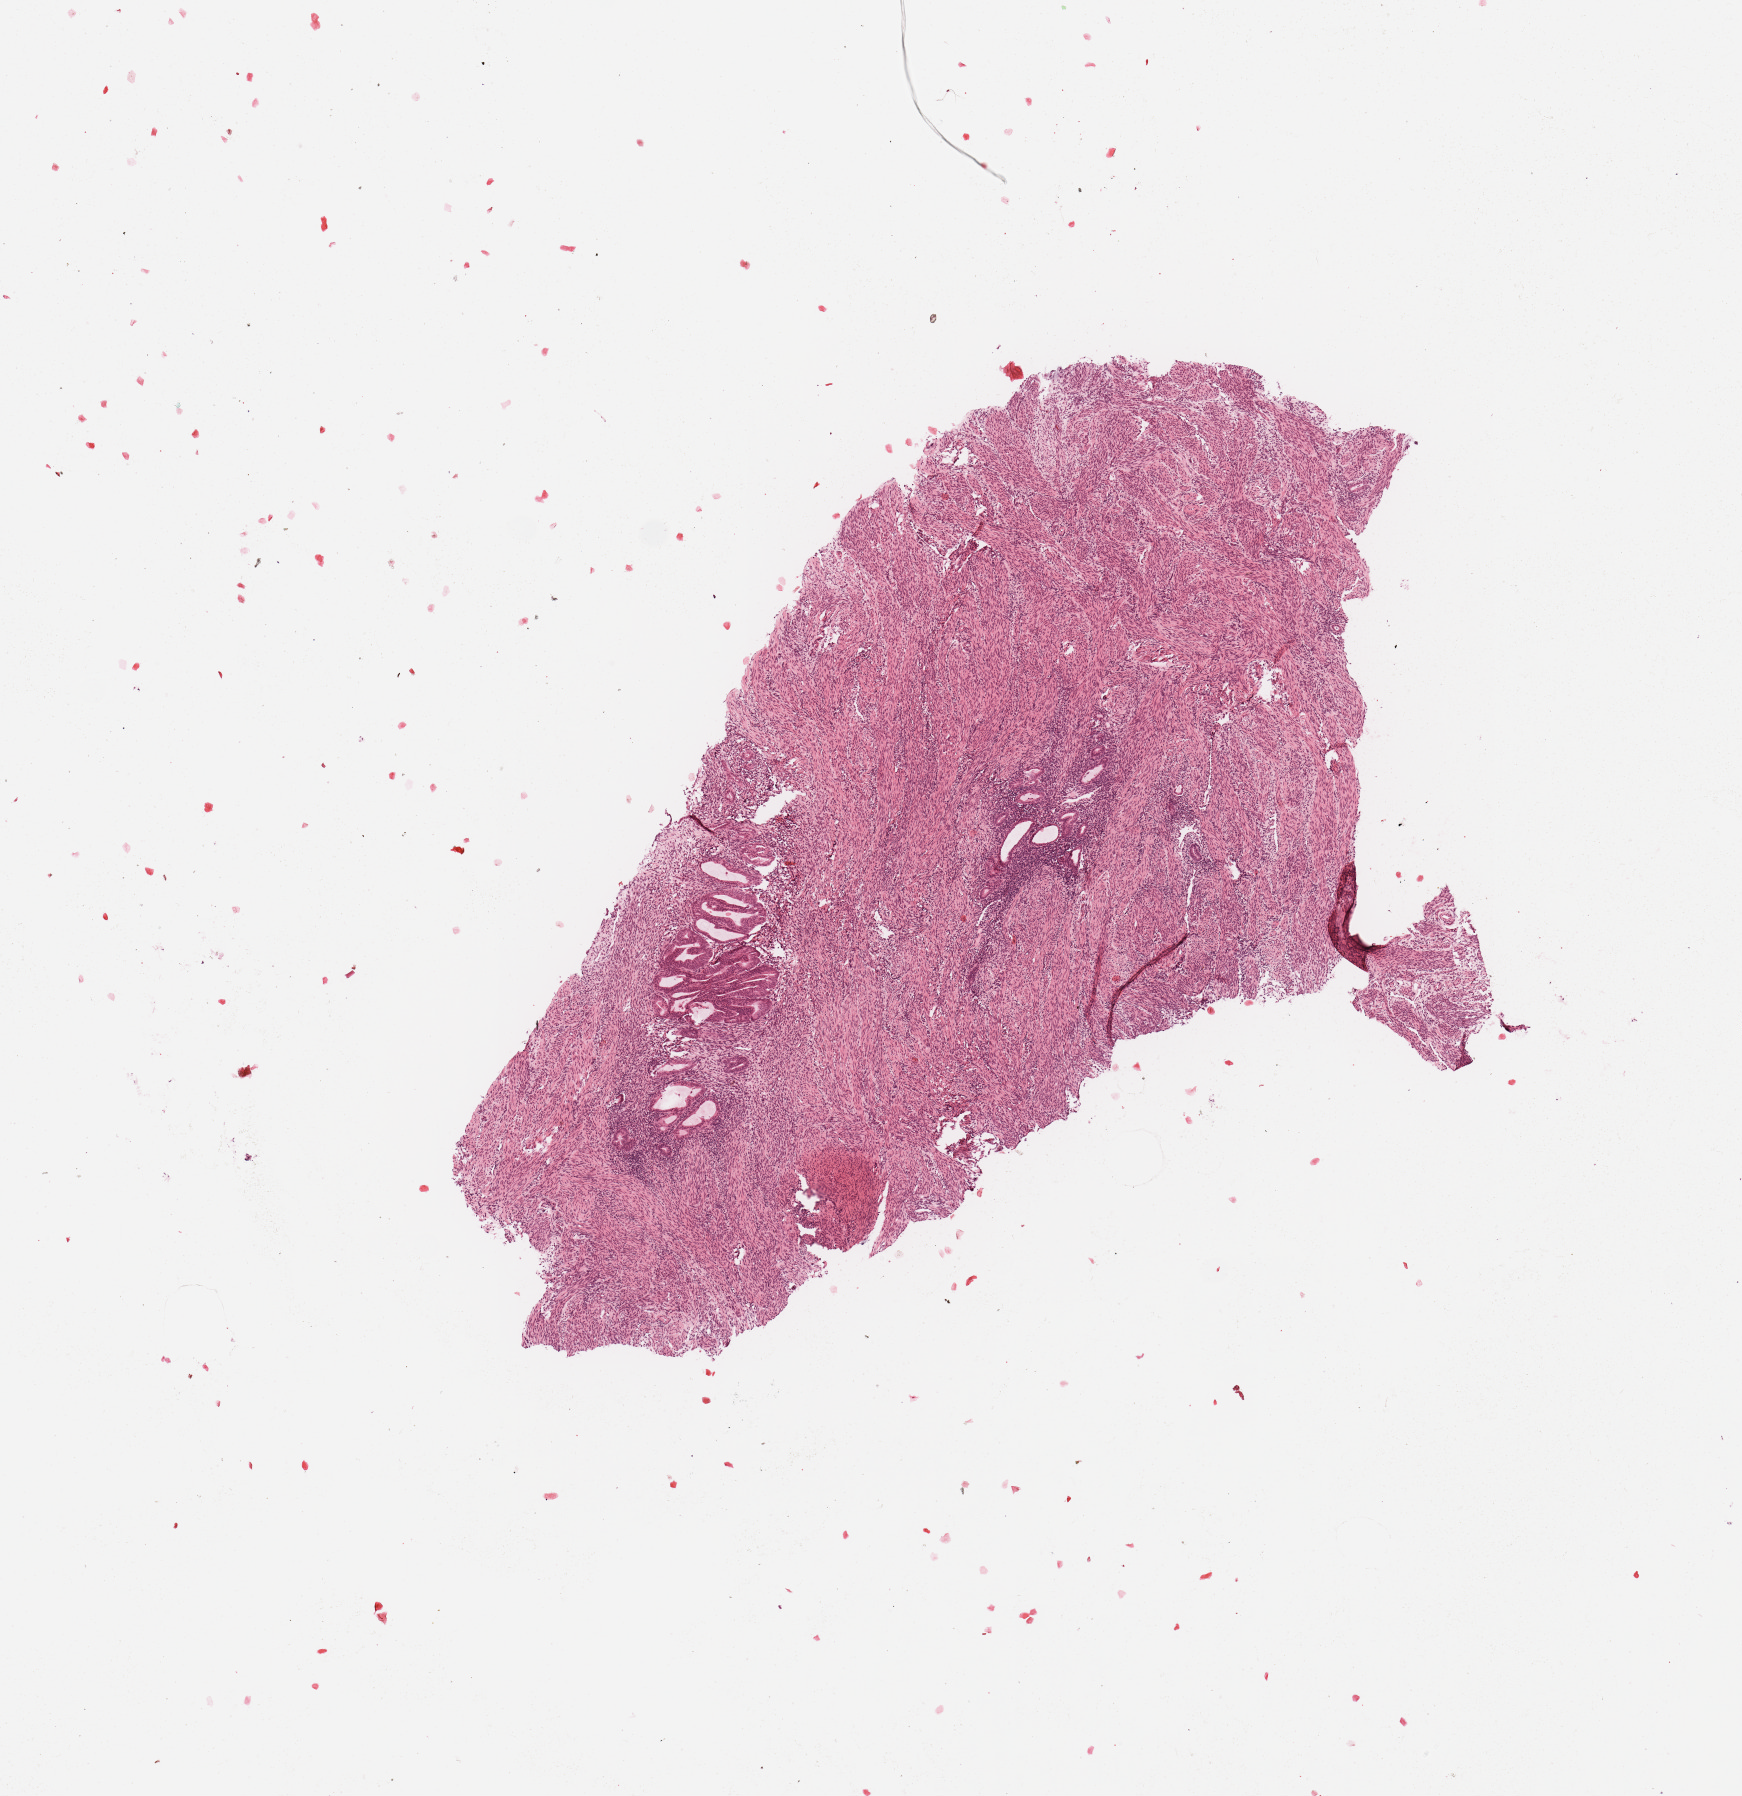
Whole-slide histology image, H&E-stained, a low-resolution overview of the entire scanned area, about 6.9 x 7.1 mm (slide scanned at 20x); uterus, normal (non-tumour) tissue. 57-year-old female patient.
This section: normal (non-tumour) tissue from the same patient. Patient diagnosis: Endometrioid adenocarcinoma, NOS.